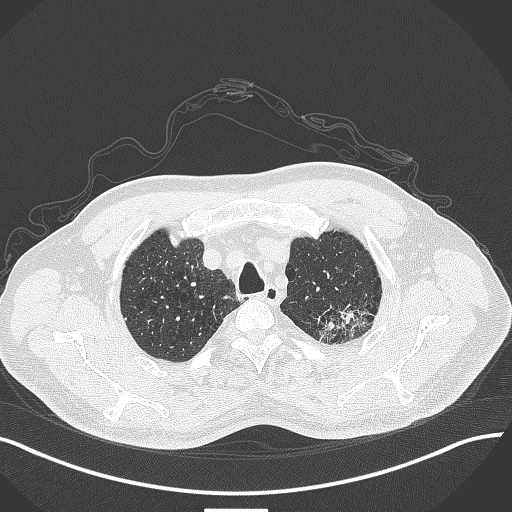
Chest CT, one axial slice; slice 359 of 429 in the series (ordered by position); reconstruction kernel B70f; 120 kVp; lung window (W 1500 / L -600 HU); 1 mm slice thickness; 512 × 512 image matrix, field of view 400 × 400 mm. Male patient, age 55 years. From the clinical record (not read from this slice): clinical TNM (as recorded): T3 N0 M1c.
Structures marked on this image (bounding box drawn by a radiologist):
- lung tumour (recorded histology: adenocarcinoma): box from (x=310, y=293) to (x=382, y=346) px